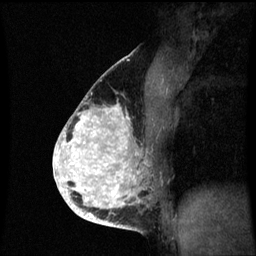
Breast MRI (dynamic contrast-enhanced), one sagittal slice; slice 38 of 60 in the series (ordered by position); dynamic contrast-enhanced series, image 2 of 3 at this slice position (ordered by acquisition); 1.5 T; TE 4.2 ms, TR 8.9 ms; 2 mm slice thickness; 256 × 256 image matrix, field of view 200 × 200 mm. Patient: female, 35 years. Case-level facts recorded for this patient, not image findings: setting: breast cancer imaged before/during neoadjuvant chemotherapy; receptor status: HR-positive, HER2-negative.
Structures marked on this image (semi-automatically segmented with operator editing):
- analysis volume of interest (the breast-tissue region the enhancement analysis was run in; not a lesion): box from (x=66, y=96) to (x=156, y=215) px
- tumour enhancement mask (voxels above the 70 % enhancement threshold inside the analysis volume of interest): (x=66, y=104)–(x=137, y=215)